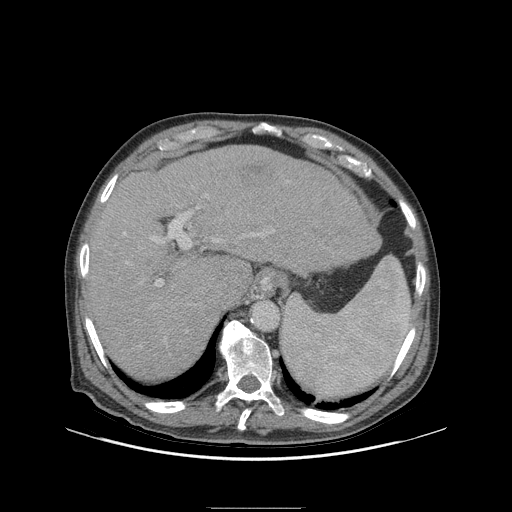
Contrast-enhanced abdominal CT (liver protocol), one axial slice. Position 73 of 105 along the scan axis. Soft-tissue window (W 400 / L 40 HU). 2.5 mm slice thickness. 512 × 512 image matrix. From the clinical record (not read from this slice): diagnosis: hepatocellular carcinoma (patient treated with transarterial chemoembolisation; whether this scan precedes or follows treatment is not stated here); TNM stage (as recorded): Stage-I; Child-Pugh class: A; tumour nodularity: uninodular; tumour size: 5.1 cm.
Structures marked on this image (semi-automatic segmentation, software-assisted and operator-edited):
- liver parenchyma outside the tumour (the mass and vessels are separate outlines, so this box may not span the whole liver): bounding box <86,144,380,380> (left, top, right, bottom; pixels)
- mass: <241,161,265,180>
- liver vessels: <124,207,256,287>